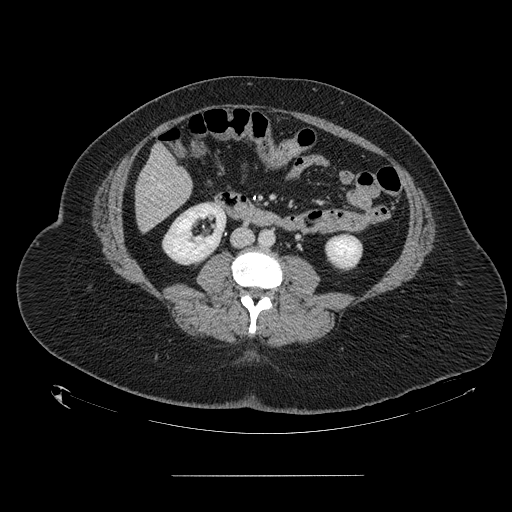
Contrast-enhanced abdominal CT, one axial slice; position 35 of 164 along the scan axis; intravenous contrast given; soft-tissue window (W 400 / L 40 HU); 2.5 mm slice thickness; 512 × 512 image matrix, field of view 495 × 495 mm. Female patient, age 52 years. From the clinical record (not read from this slice): diagnosis: colorectal cancer liver metastases, imaged before liver resection; multiple liver metastases: yes; largest metastasis: 3.5 cm; disease in both lobes: no.
Structures marked on this image (manually delineated by an expert):
- hepatic veins: bounding box <151,177,161,187> (left, top, right, bottom; pixels)
- liver: <136,147,192,230>